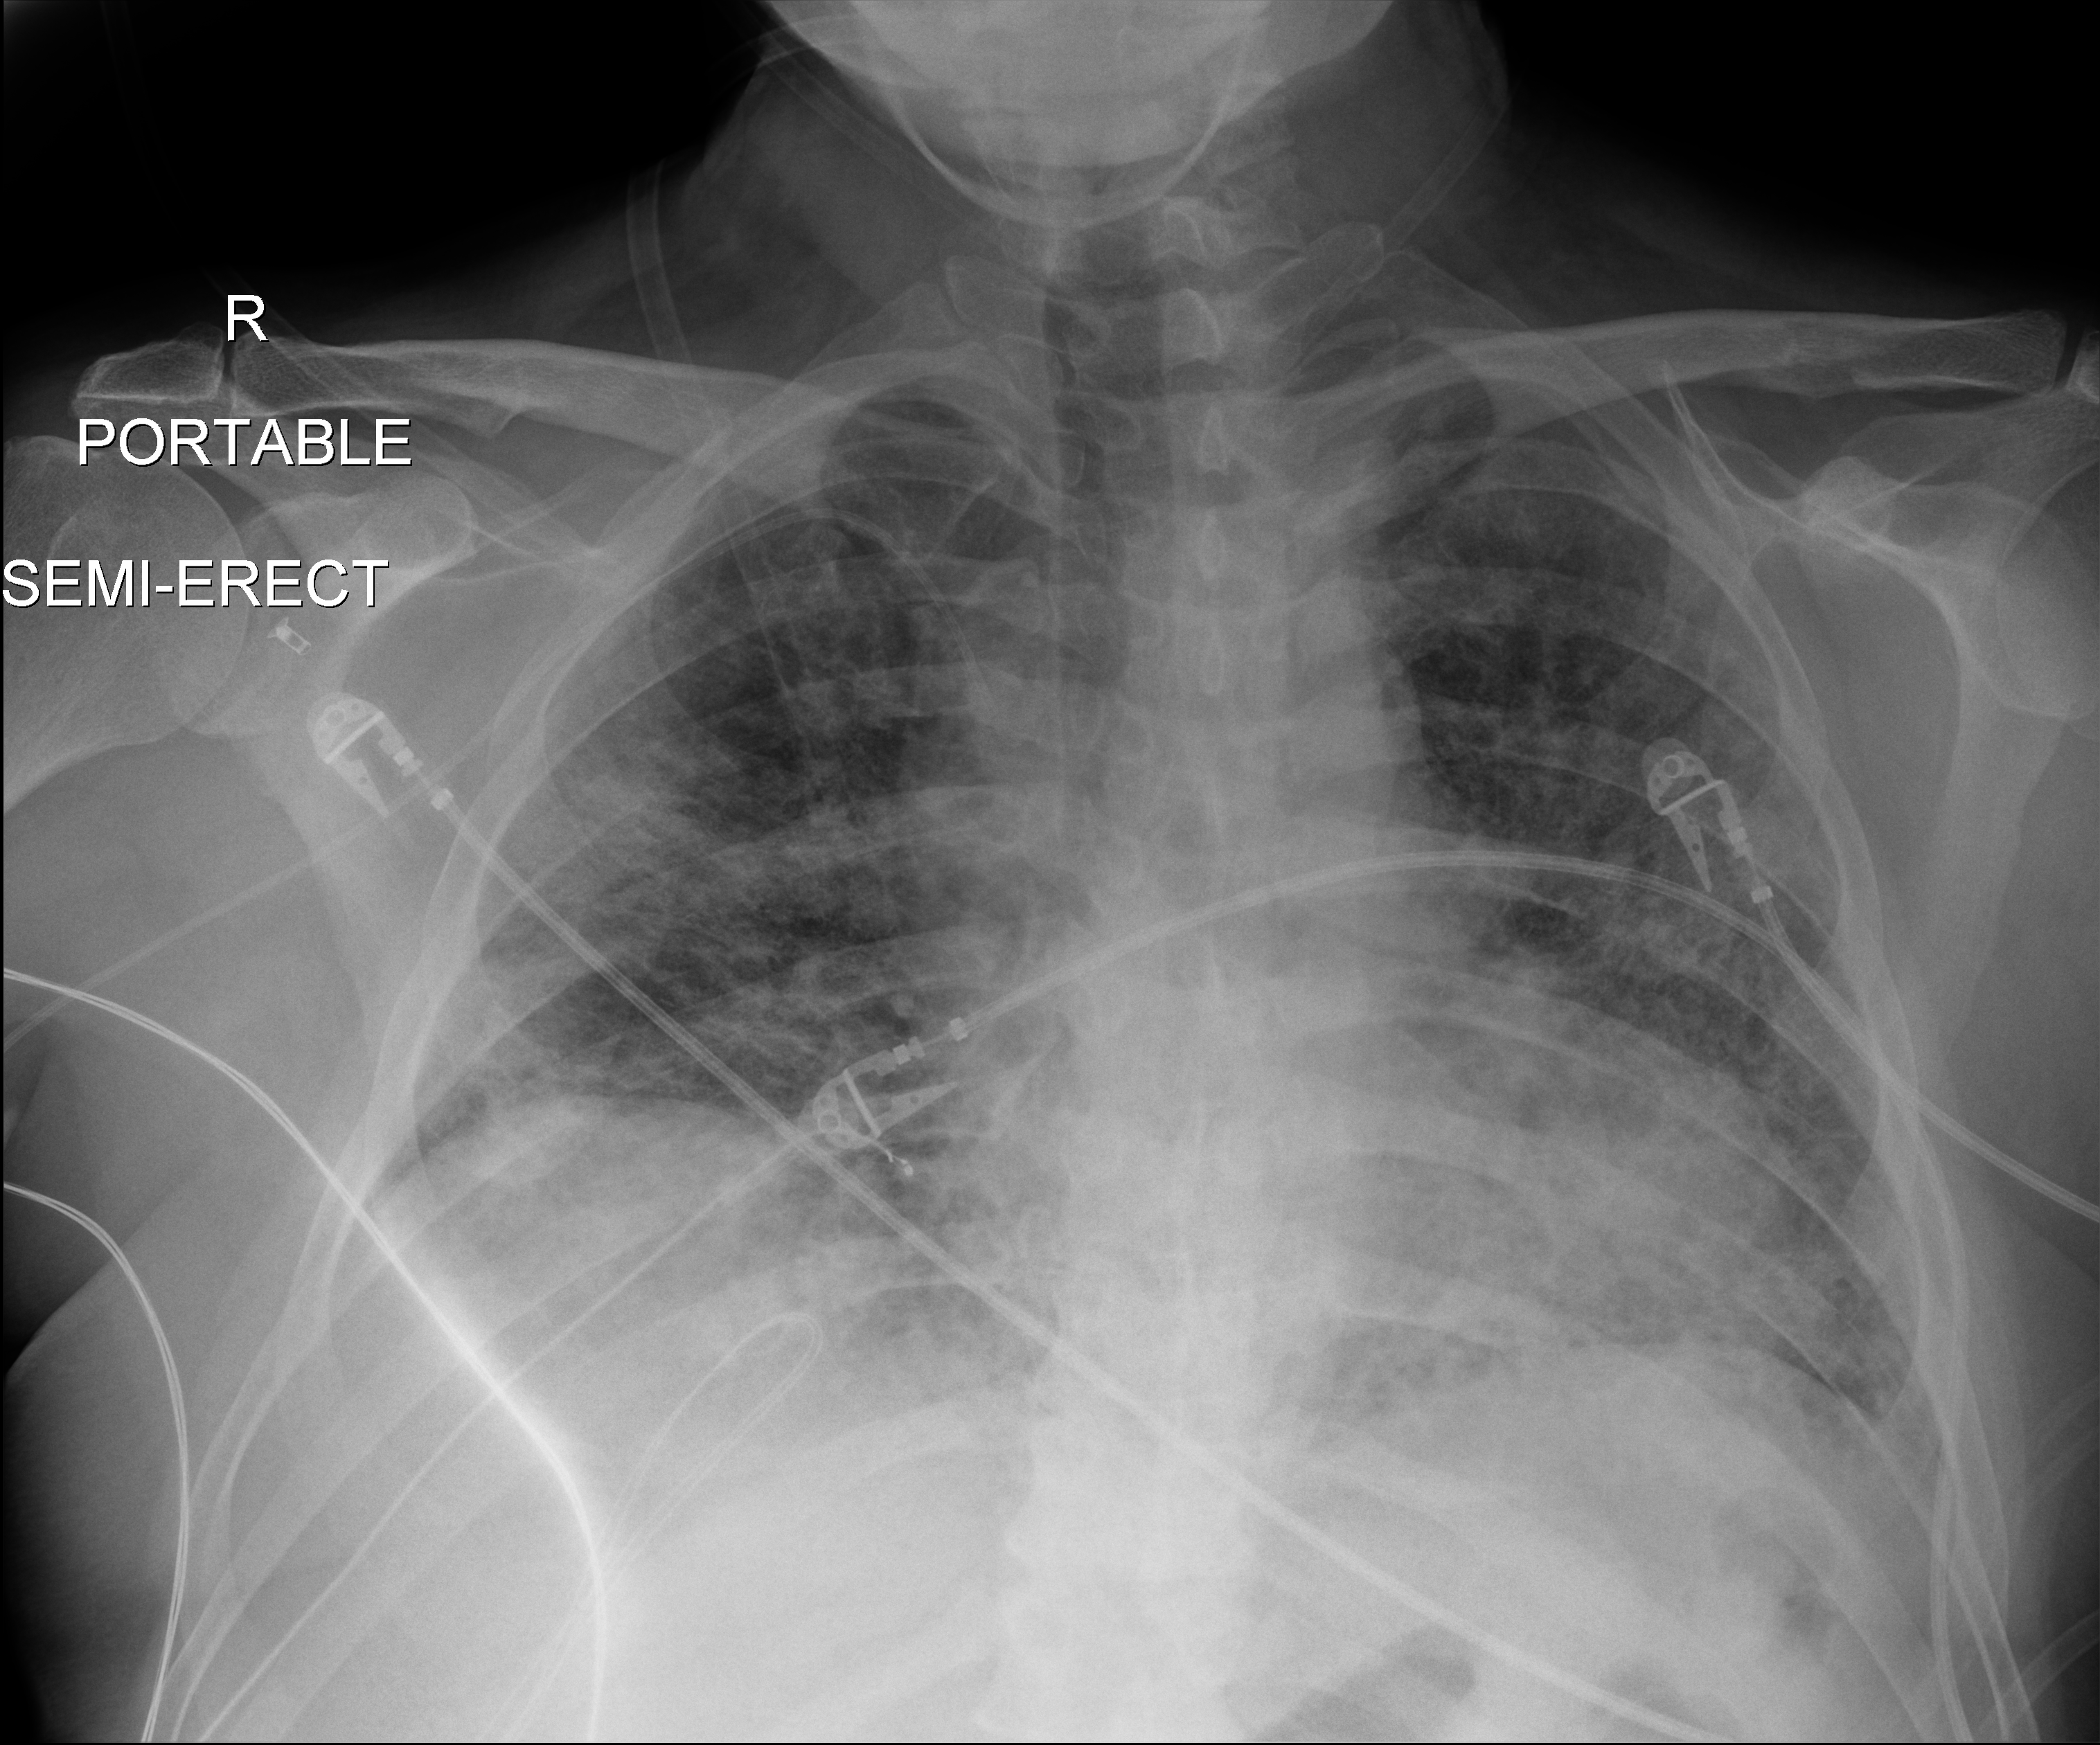
Chest X-ray, anteroposterior (AP) projection. Patient hospitalised with COVID-19; male, aged 18–59 years.
From the hospital-stay record, not from the radiograph (when in the stay this image was taken is not recorded): length of hospital stay: 52 days.